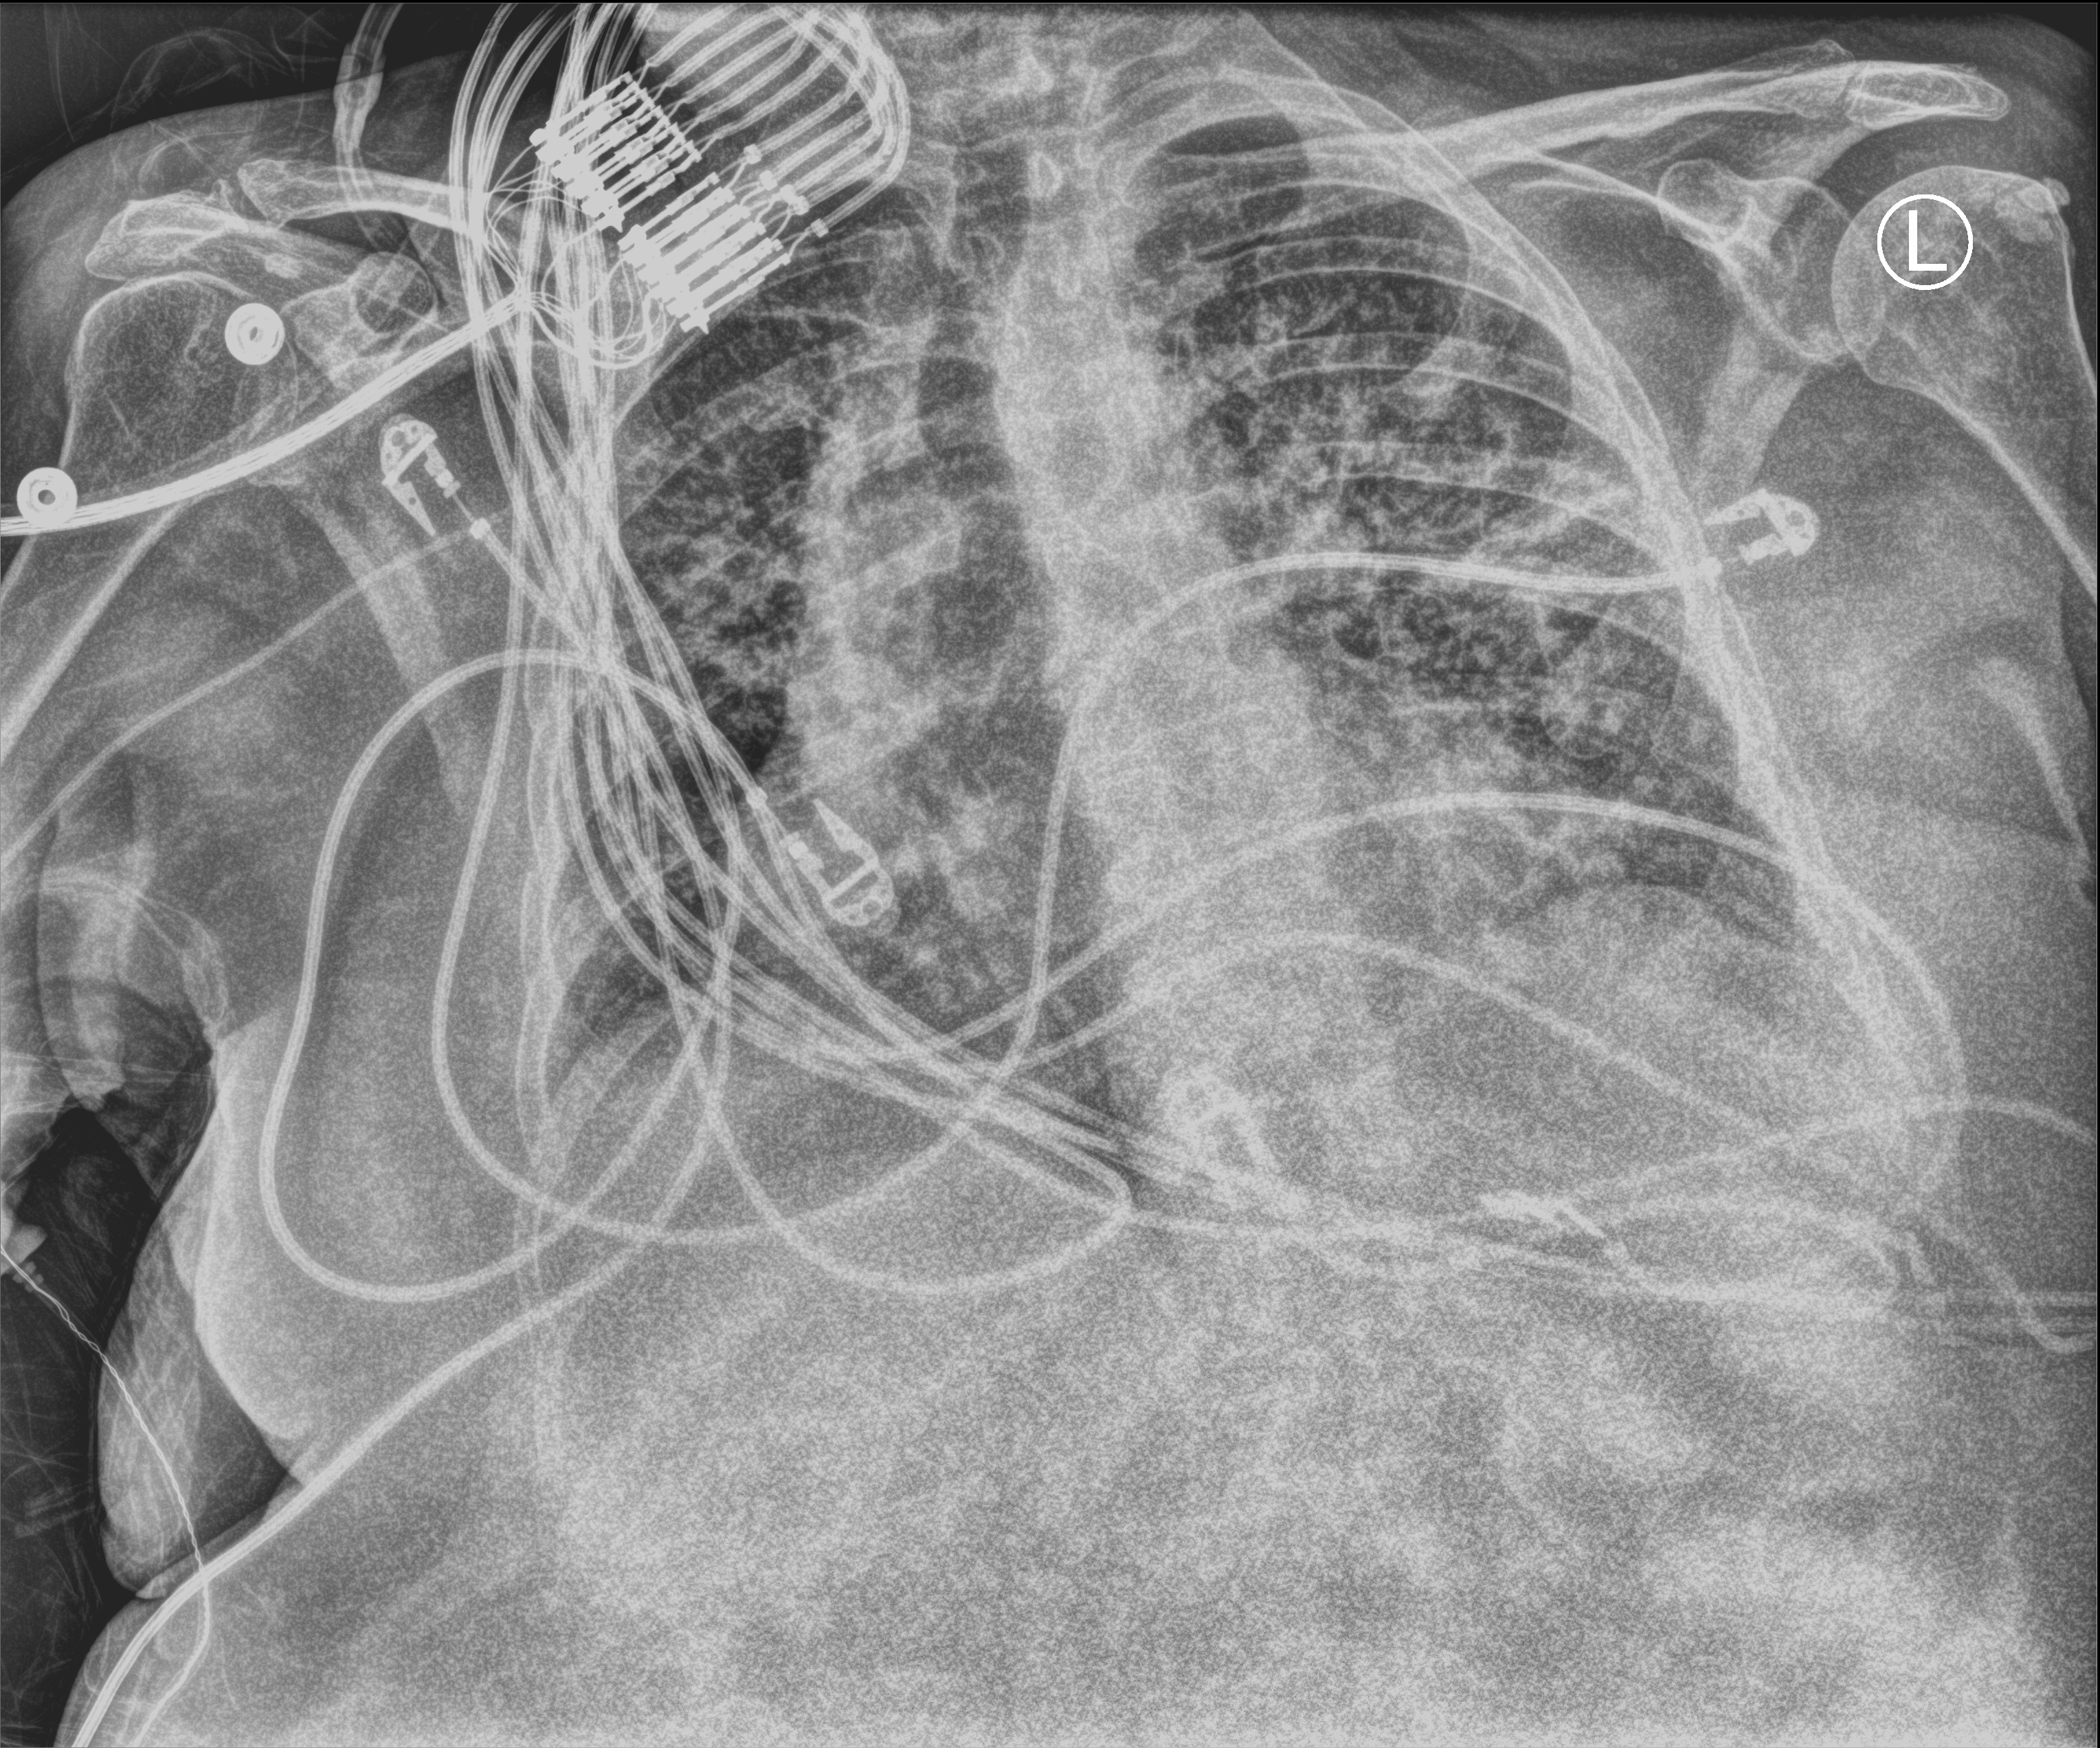
Chest X-ray (portable); anteroposterior (AP) projection. Patient hospitalised with COVID-19; female, aged 75–90 years.
From the hospital-stay record, not from the radiograph (when in the stay this image was taken is not recorded):
- smoking status (admission record): former
- mechanically ventilated during this hospital stay: yes
- length of hospital stay: 31 days